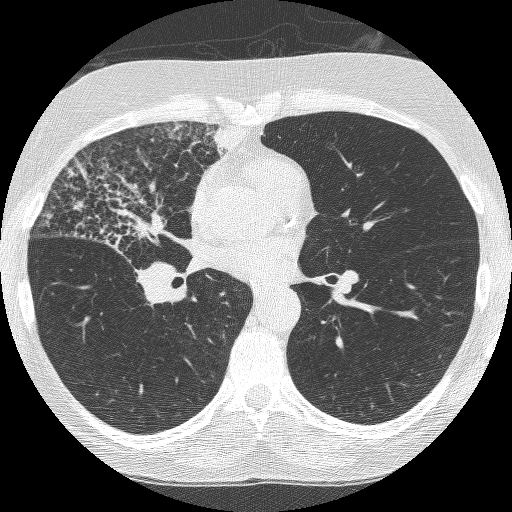
Chest CT (low-dose screening protocol), one axial image; third annual screen; lung window (W 1500 / L -600 HU); 1.25 mm slice thickness; slice 134 of 253 in the series. Female, age 64 years at enrolment. Former smoker at enrolment.
Lesion marked by an expert reader, box from (x=57, y=164) to (x=200, y=310) px. The exam's reader record, not a measurement of the box and not confirmed to be the same lesion: non-calcified nodule or mass ≥4 mm, right upper lobe, 49 × 43 mm, spiculated (stellate) margins, soft tissue attenuation, pre-existing on the prior screen: yes; interval growth: yes. Official screen result: positive, other. Later outcome: lung cancer diagnosed 7 days after this screen — adenocarcinoma, NOS, right upper lobe, right middle lobe, right hilum, stage IV (AJCC 6th edition), 85 mm at pathology.